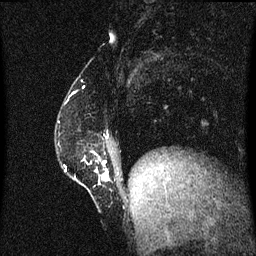
Breast MRI (dynamic contrast-enhanced), one sagittal slice; position 14 of 60 along the scan axis; dynamic contrast-enhanced series, image 2 of 3 at this slice position (ordered by acquisition); 1.5 T; TE 4.2 ms, TR 8.4 ms; 2 mm slice thickness; 256 × 256 image matrix. Patient: female, 52 years. Case-level facts recorded for this patient, not image findings: setting: breast cancer imaged before/during neoadjuvant chemotherapy; receptor status: HER2-positive.
Outlined on this slice (semi-automatically segmented with operator editing):
- analysis volume of interest (the breast-tissue region the enhancement analysis was run in; not a lesion): bounding box <66,144,113,197> (left, top, right, bottom; pixels)
- tumour enhancement mask (voxels above the 70 % enhancement threshold inside the analysis volume of interest): <97,162,110,181>